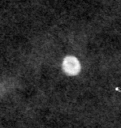
Cropped region of a digitized screen-film mammogram centred on a radiologist-marked abnormality; left breast; MLO view.
Calcifications, morphology lucent centered; BI-RADS assessment category 2; benign without callback (not worked up further).